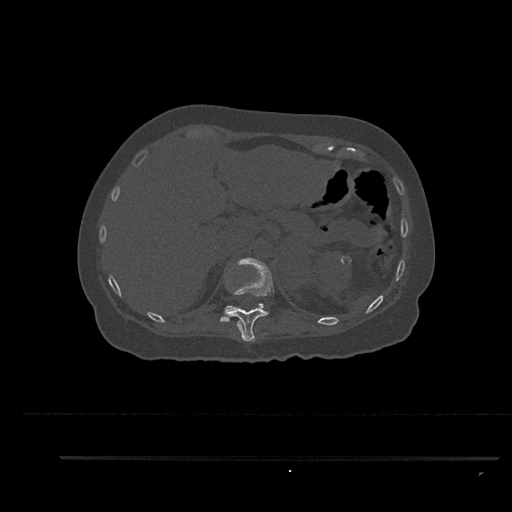
CT including the spine, one axial slice; slice 299 of 797 in the series (ordered by position); 120 kVp; bone window (W 1800 / L 400 HU); 0.5 mm slice thickness; 512 × 512 image matrix. Female patient, age 44 years. Case-level facts recorded for this patient, not image findings: primary cancer: renal.
Annotated regions visible in this slice (semi-automatic segmentation, software-assisted and operator-edited):
- T11 vertebra: bounding box [x1, y1, x2, y2] px = [227, 258, 275, 342]
- T12 vertebra: [220, 303, 268, 322]